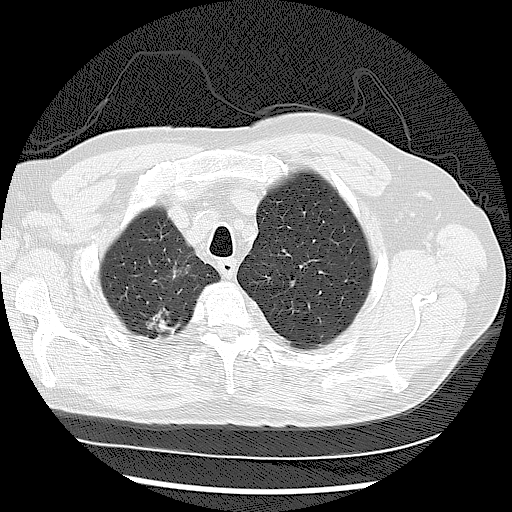
Low-dose screening chest CT, one axial slice. Slice 99 of 122 in the series (ordered by position). Lung window (W 1500 / L -600 HU). 2.5 mm slice thickness. 512 × 512 image matrix, field of view 360 × 360 mm.
Outlined on this slice (expert manual segmentation):
- lesion 1 (tumor, upper lobe of right lung): bounding box (x1, y1, x2, y2) in pixels: (146, 308, 179, 333)